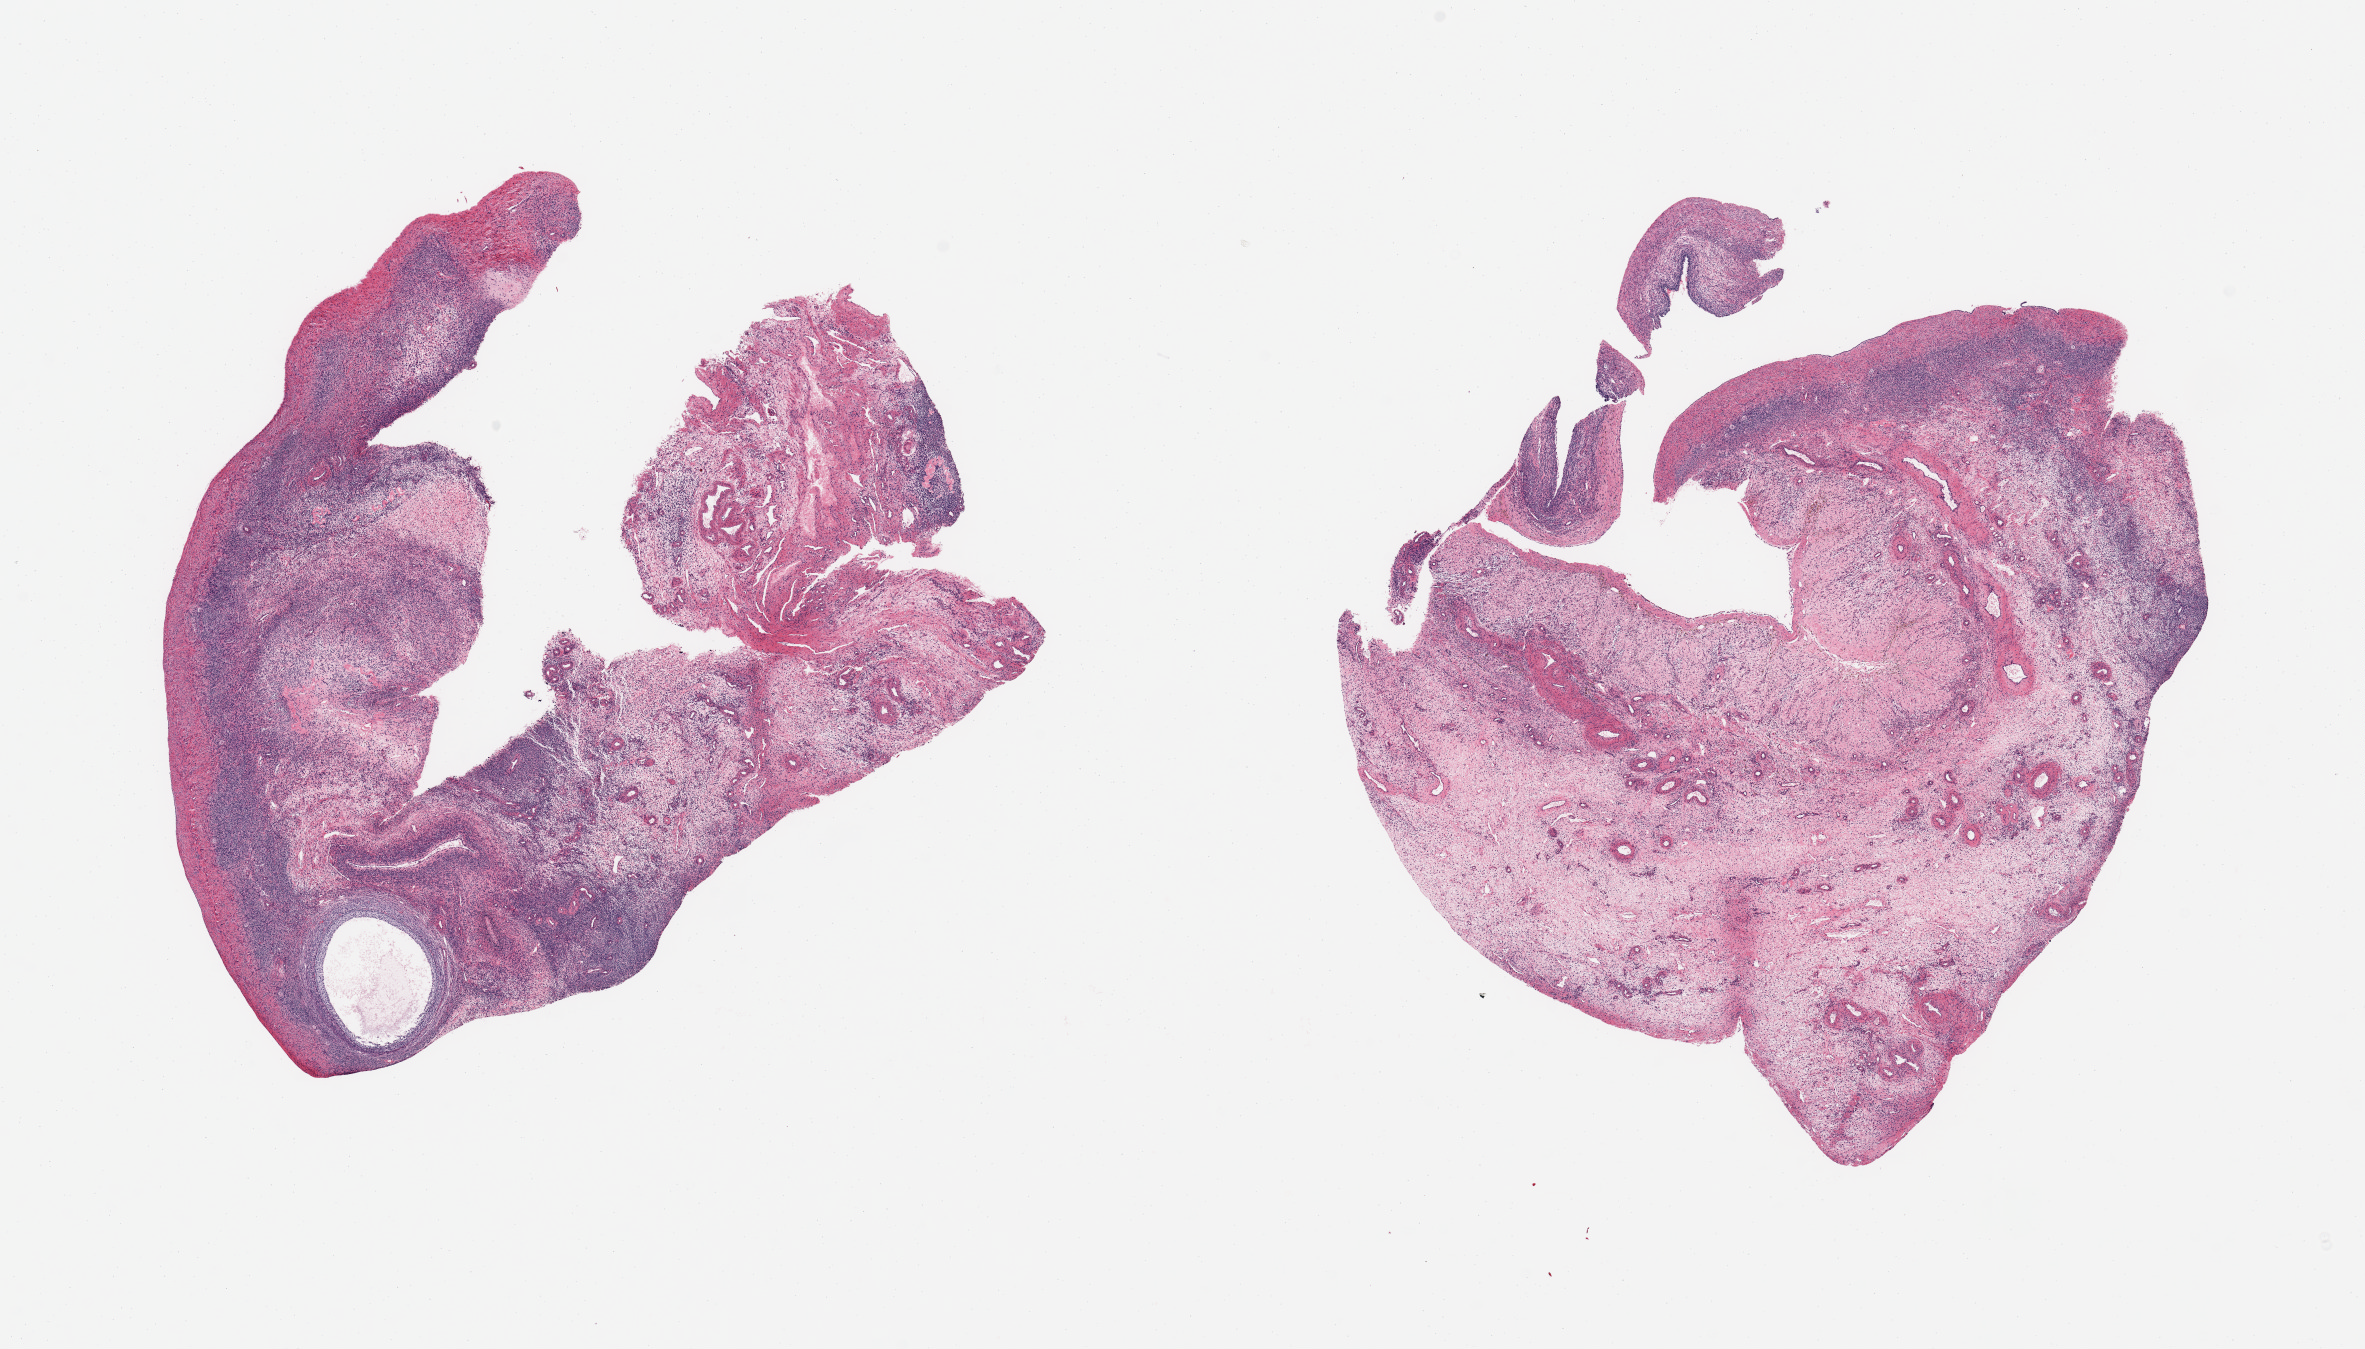
Haematoxylin and eosin whole-slide image, brightfield, shown as a low-resolution overview of the whole scanned area (about 18.7 x 10.7 mm). PAXgene-fixed, paraffin-embedded tissue. Target tissue: ovary. Donor tissue sample. Female donor.
Reviewer comment on this tissue sample: 2 pieces; large corpus luteum occupies 70% of 1 piece and 30% of the other.